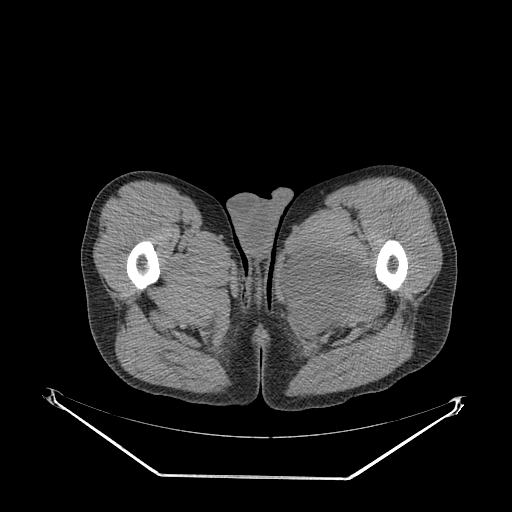
CT of an extremity soft-tissue mass (from a PET/CT study), one axial slice. Position 39 of 267 along the scan axis. 140 kVp. Soft-tissue window (W 400 / L 40 HU). 3.75 mm slice thickness. 512 × 512 image matrix, field of view 500 × 500 mm. Male patient. Case-level facts recorded for this patient, not image findings: histological type: pleiomorphic liposarcoma; grade: high; site of the primary tumour: left thigh.
Outlined on this slice (expert contour drawn on MRI and transferred to this co-registered scan by the dataset authors):
- gross tumour volume including surrounding oedema: bounding box [x1, y1, x2, y2] px = [285, 242, 360, 328]
- gross tumour volume (mass): [288, 247, 355, 312]